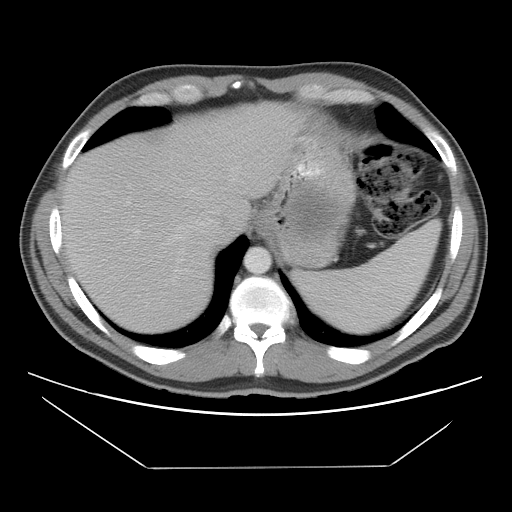
Contrast-enhanced abdominal CT, one axial slice; slice 83 of 131 in the series (ordered by position); reconstruction kernel STANDARD; intravenous contrast given; soft-tissue window (W 400 / L 40 HU); 5 mm slice thickness; 512 × 512 image matrix, field of view 396 × 396 mm. Male patient, age 44 years. From the clinical record (not read from this slice): diagnosis: adrenocortical carcinoma; tumour side: left adrenal; tumour size at pathology: 15.5 cm; Ki-67 index: 6 %; stage (as recorded): 2.
Outlined on this slice (semi-automatic segmentation, software-assisted and operator-edited):
- mass: bounding box <290,192,331,241> (left, top, right, bottom; pixels)